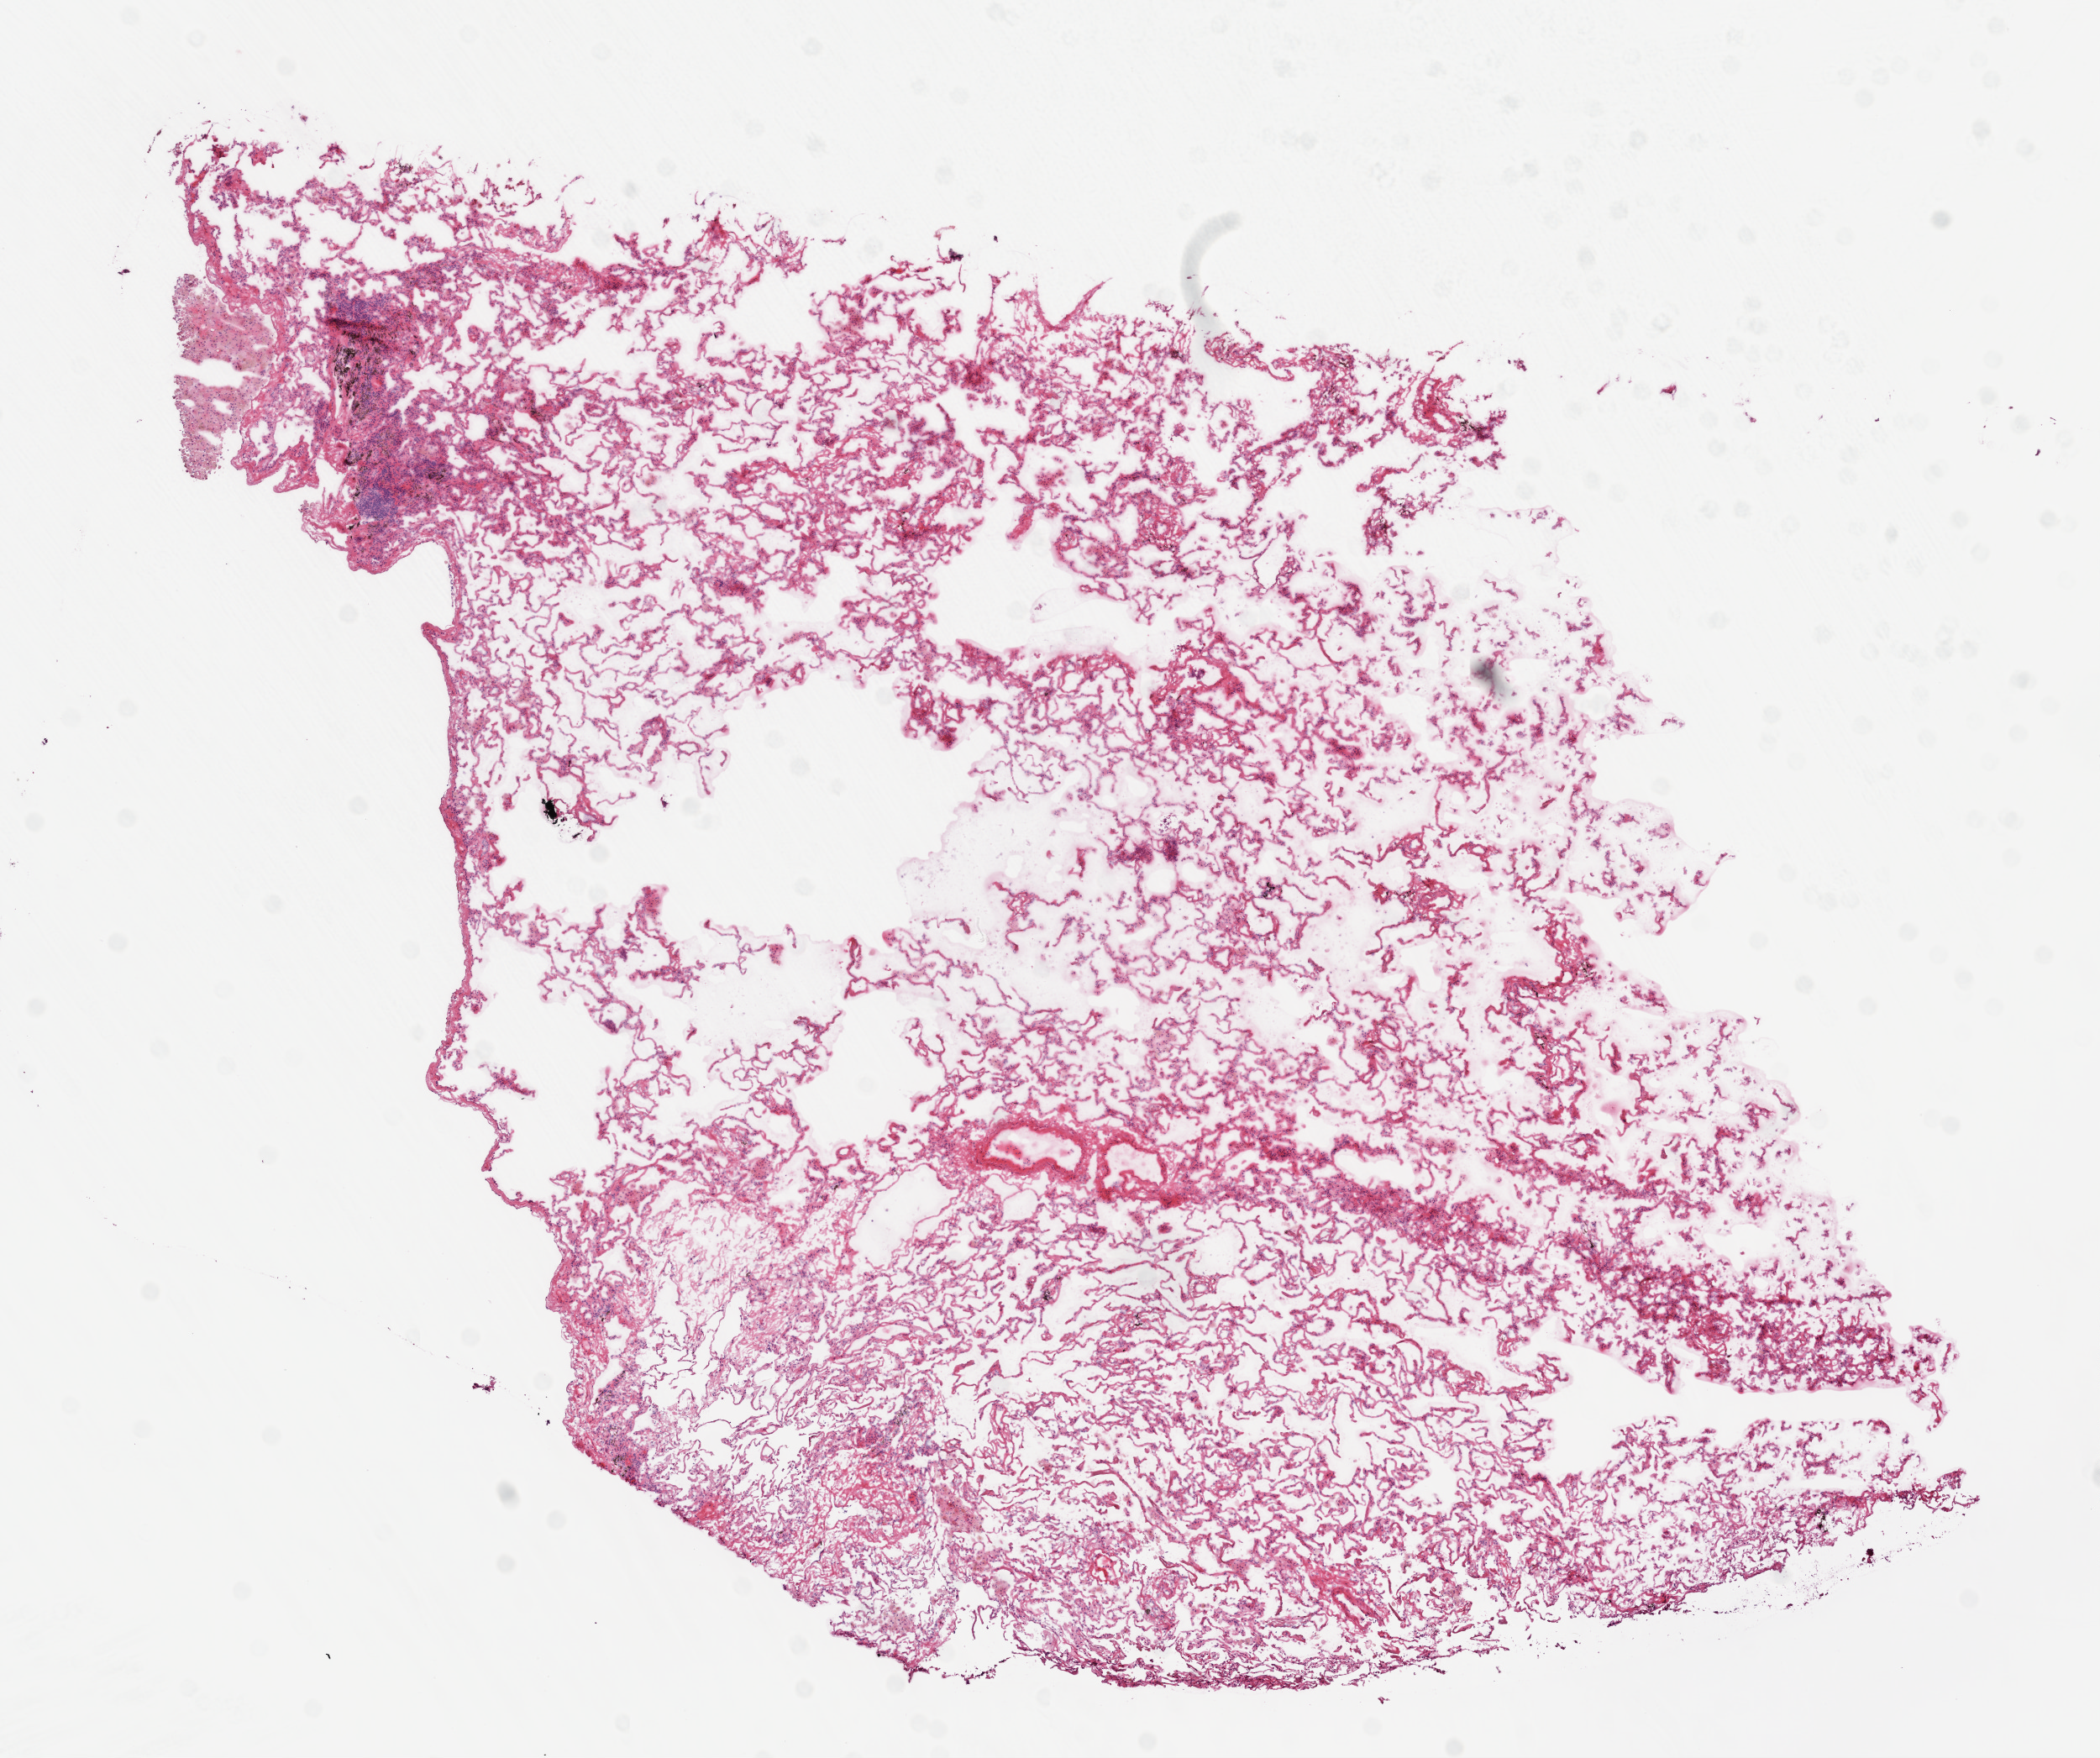
Whole-slide histology image, H&E — whole scanned area (about 10.0 x 8.4 mm, from a 20x scan) shown as a low-resolution overview; frozen section from the top of the tissue portion; sample: solid tissue normal (non-tumour tissue), lung. Patient: female, age at initial diagnosis 72 years.
This section: solid tissue normal sample (biorepository sample class). Patient diagnosis: Squamous cell carcinoma, NOS (lower lobe, lung).